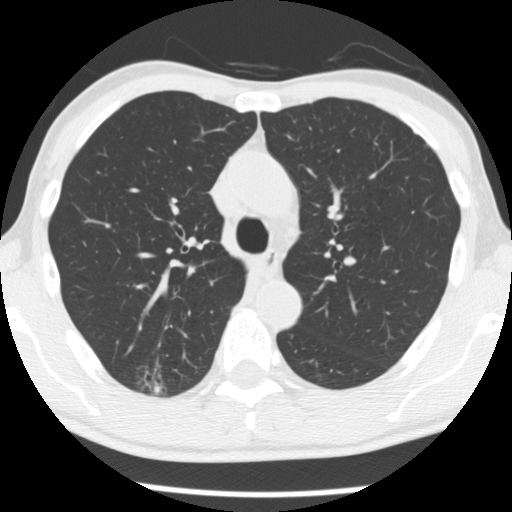
Low-dose screening chest CT, axial slice; first (baseline) screen; lung window (W 1500 / L -600 HU); 2.5 mm slice thickness; 120 kVp; 512 × 512 image matrix. Male, age 66 years at enrolment. Former smoker at enrolment.
• Expert-annotated lung lesion, bounding box (x1, y1, x2, y2) in pixels: (130, 356, 191, 404).
• The screening reader recorded 4 non-calcified nodules or masses ≥4 mm on this exam (right upper lobe, right upper lobe, right upper lobe, left lower lobe); which of them this box marks is not recorded.
• Official screen result: positive, change unspecified: nodule(s) >= 4 mm or enlarging nodule(s), mass(es), or other non-specific abnormalities suspicious for lung cancer.
• Participant outcome: lung cancer diagnosed 503 days after this screen — adenocarcinoma, NOS, right upper lobe, undifferentiated (G4), stage IA (AJCC 6th edition), 20 mm at pathology.